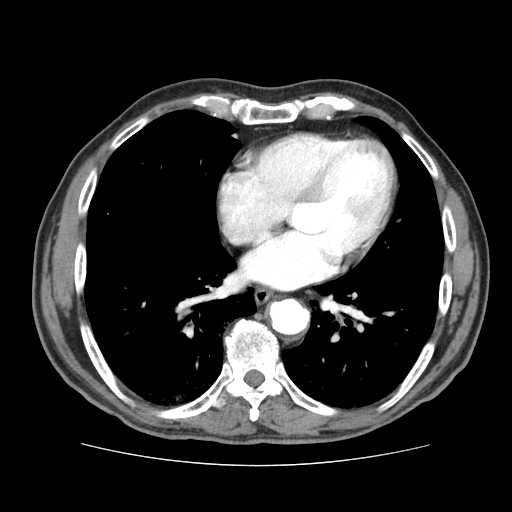
Contrast-enhanced abdominal CT (liver protocol), one axial slice; position 79 of 79 along the scan axis; reconstruction kernel STANDARD; 120 kVp; soft-tissue window (W 400 / L 40 HU); 2.5 mm slice thickness; 512 × 512 image matrix, field of view 360 × 360 mm. Case-level facts recorded for this patient, not image findings: diagnosis: hepatocellular carcinoma (patient treated with transarterial chemoembolisation; whether this scan precedes or follows treatment is not stated here); TNM stage (as recorded): Stage-I; Child-Pugh class: A; tumour nodularity: uninodular.
Outlined on this slice (semi-automatic segmentation, software-assisted and operator-edited):
- abdominal aorta: box from (x=270, y=299) to (x=308, y=333) px